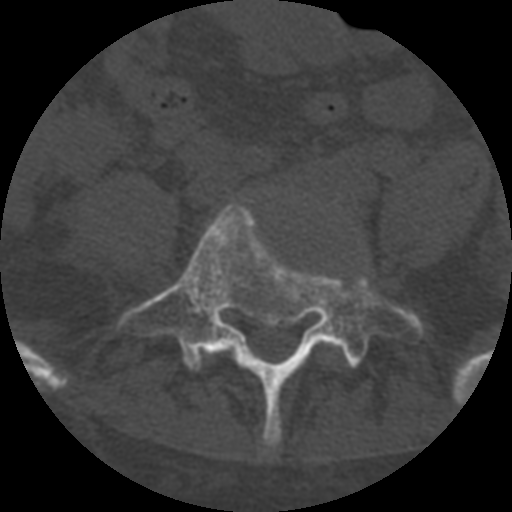
CT including the spine, one axial slice. Slice 189 of 708 in the series (ordered by position). Reconstruction kernel STANDARD. One of 3 acquisitions stored at this slice position. Bone window (W 1800 / L 400 HU). 1.25 mm slice thickness. 512 × 512 image matrix, field of view 160 × 160 mm. Patient age 55 years. From the clinical record (not read from this slice): primary cancer: colon; vertebrae with lytic lesions (as recorded): T12, L1, L5.
Structures marked on this image (semi-automatically segmented with operator editing):
- L5 vertebra: box from (x=119, y=204) to (x=423, y=446) px